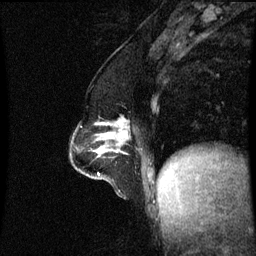
Breast MRI (dynamic contrast-enhanced), one sagittal slice. Position 25 of 60 along the scan axis. Dynamic contrast-enhanced series, image 2 of 3 at this slice position (ordered by acquisition). 1.5 T. TE 4.2 ms, TR 8.9 ms. 256 × 256 image matrix, field of view 200 × 200 mm. Female patient, age 47 years. Case-level facts recorded for this patient, not image findings: setting: breast cancer imaged before/during neoadjuvant chemotherapy; receptor status: HR-positive, HER2-negative.
Structures marked on this image (semi-automatic segmentation, software-assisted and operator-edited):
- analysis volume of interest (the breast-tissue region the enhancement analysis was run in; not a lesion): bounding box <71,122,129,163> (left, top, right, bottom; pixels)
- tumour enhancement mask (voxels above the 70 % enhancement threshold inside the analysis volume of interest): <103,122,128,141>